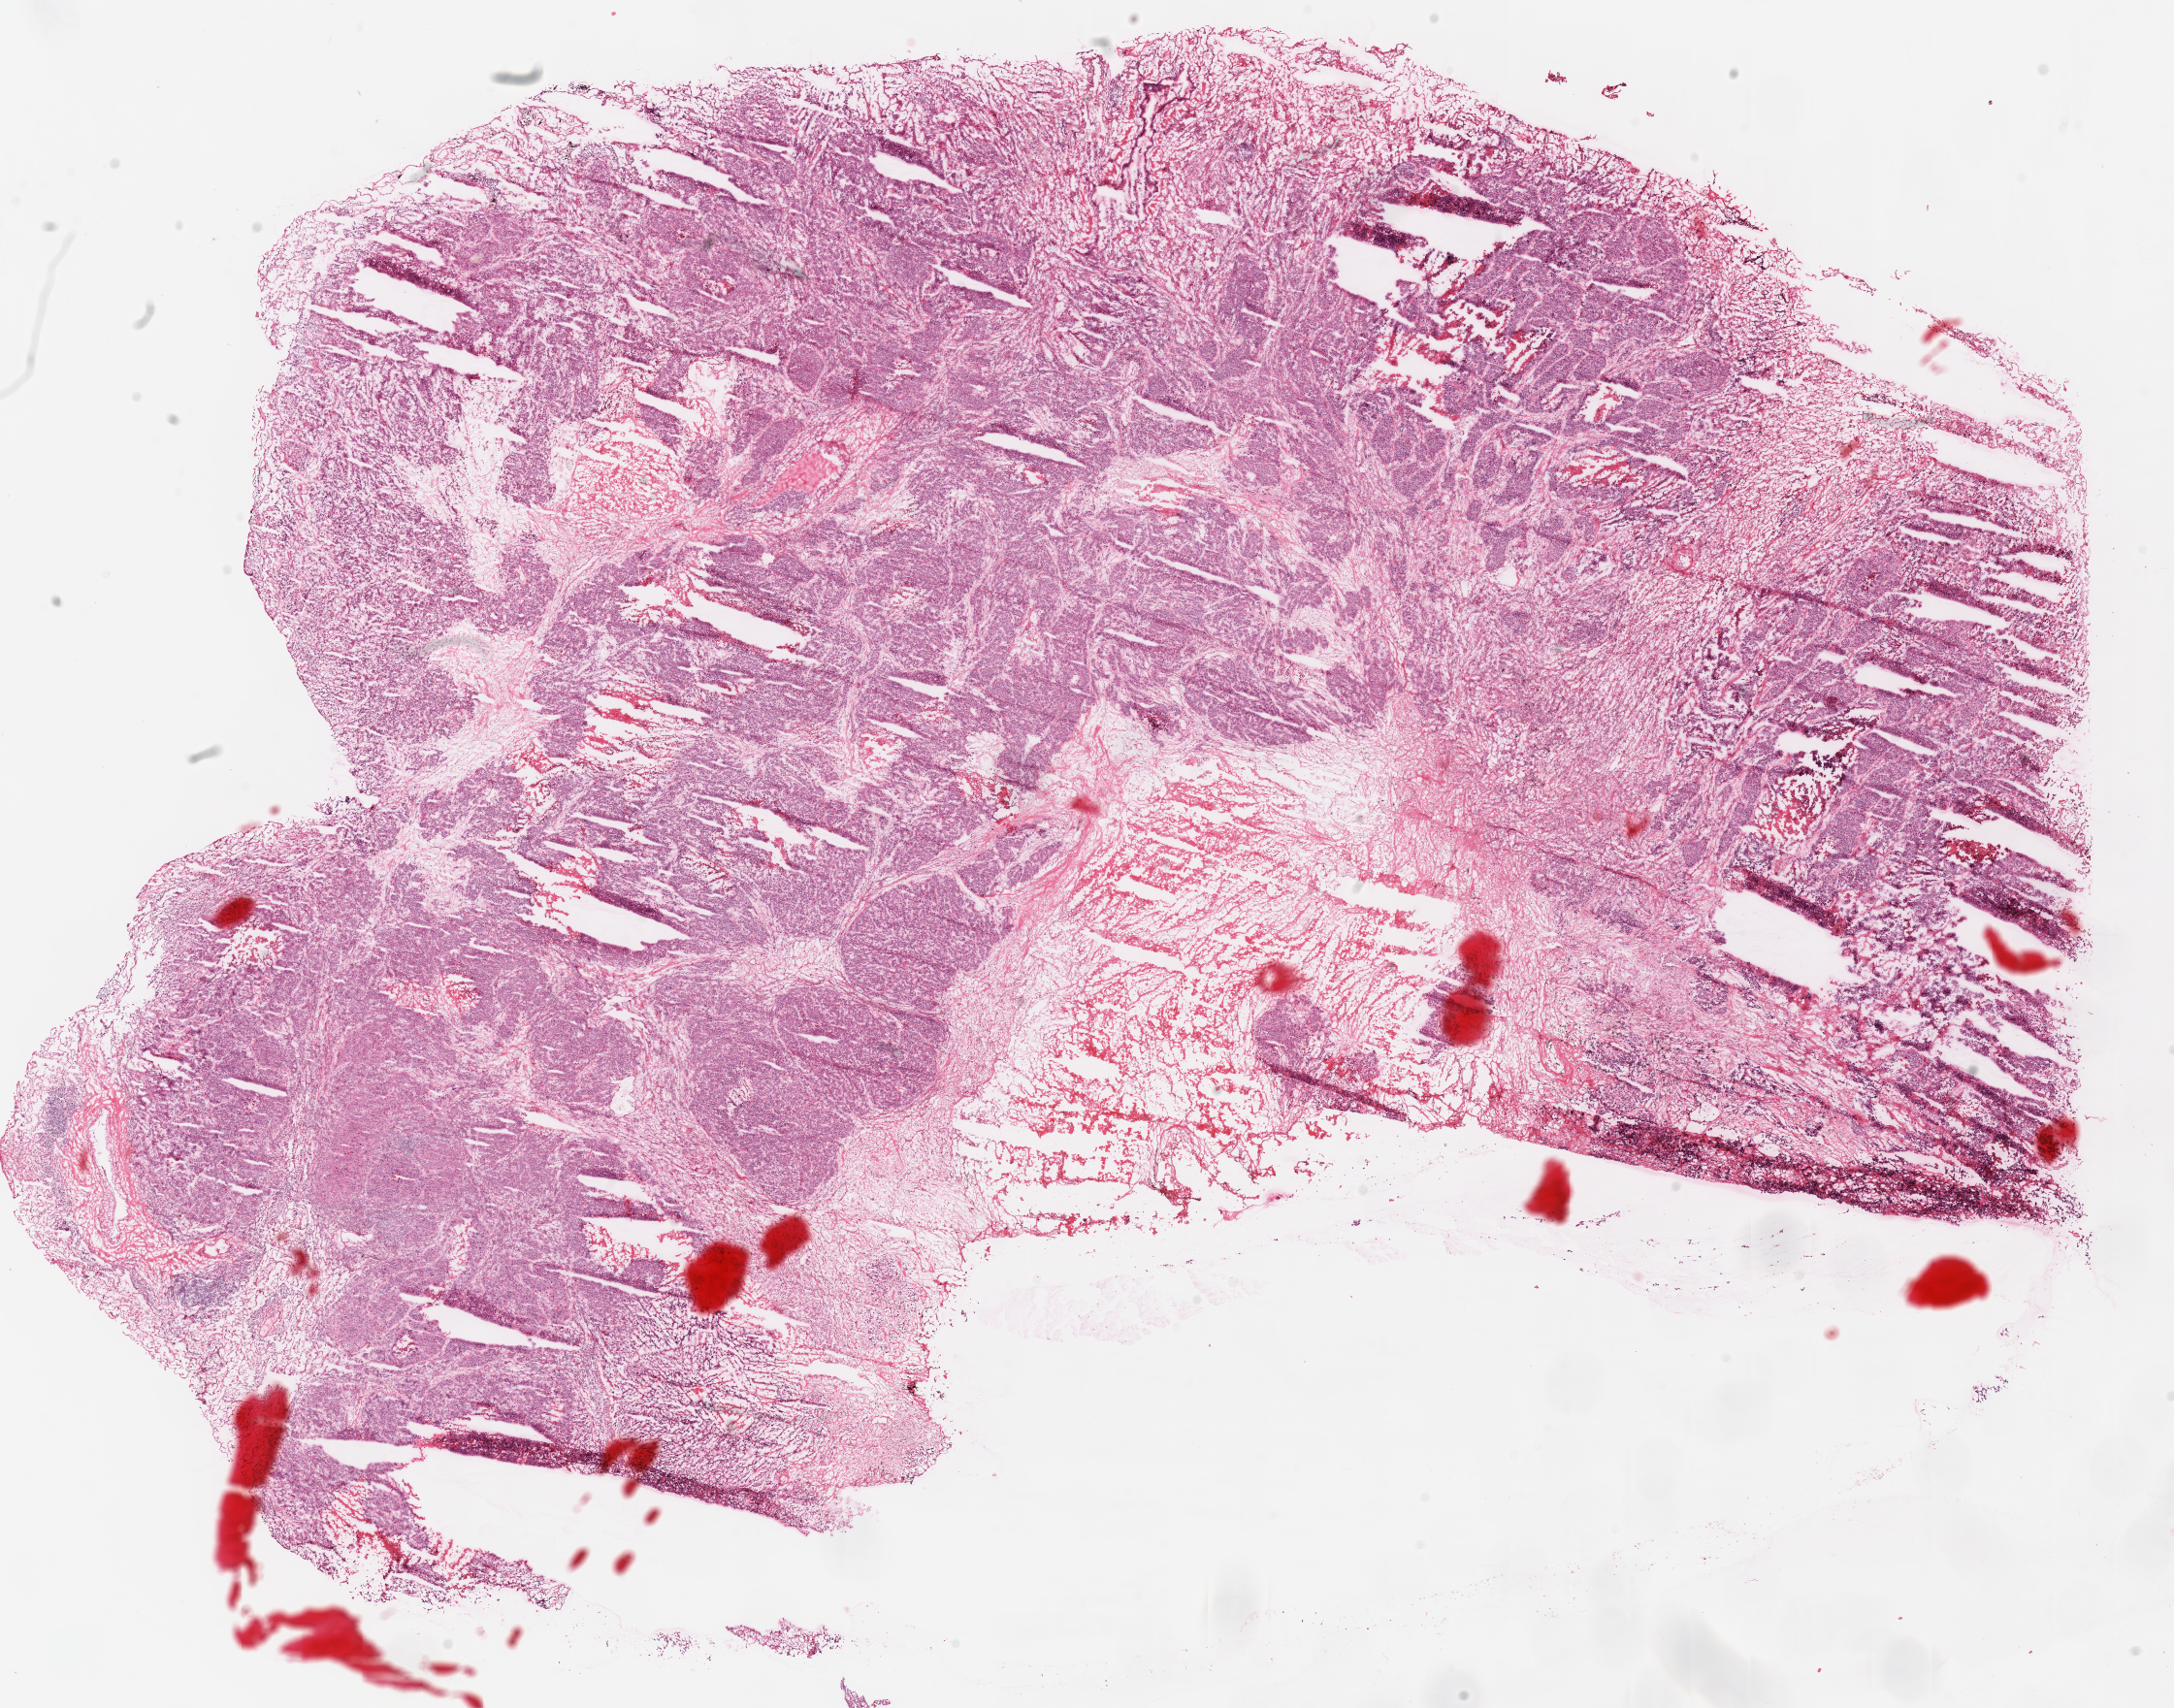
Whole-slide histology image, H&E, whole scanned area (about 17.6 x 13.8 mm) shown as a low-resolution overview; frozen section; sample: primary tumour, lung. Male, age 44 years at initial diagnosis. Slide review estimates, as recorded: tumour cells 80%, tumour nuclei 80%, normal cells 0%, stromal cells 10%, necrosis 10%.
AJCC pathologic stage: IB. Pathologic diagnosis: Adenocarcinoma, NOS (upper lobe, lung).